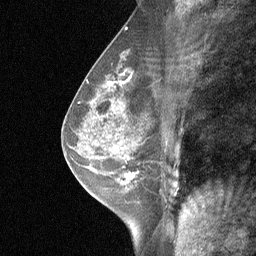
Breast MRI (dynamic contrast-enhanced), one sagittal slice. Position 34 of 64 along the scan axis. Dynamic contrast-enhanced study with each time point stored as its own series, time point 2 of 3 at this slice position (early post-contrast, ordered by acquisition time). 1.5 T. TE 4.8 ms, TR 27 ms. 2 mm slice thickness. 256 × 256 image matrix, field of view 180 × 180 mm. Female patient, age 47 years. From the clinical record (not read from this slice): setting: breast cancer imaged before/during neoadjuvant chemotherapy; receptor status: HR-positive, HER2-negative.
Outlined on this slice (semi-automatically segmented with operator editing):
- analysis volume of interest (the breast-tissue region the enhancement analysis was run in; not a lesion): bounding box [x1, y1, x2, y2] px = [104, 138, 165, 198]
- tumour enhancement mask (voxels above the 90 % enhancement threshold inside the analysis volume of interest): [113, 142, 135, 180]